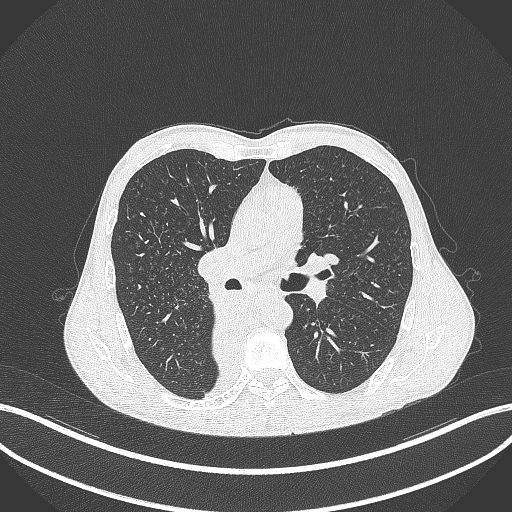
Chest CT, one axial slice. Slice 220 of 371 in the series (ordered by position). Lung window (W 1500 / L -600 HU). 512 × 512 image matrix, field of view 400 × 400 mm. Patient: male, 58 years. From the clinical record (not read from this slice): clinical TNM (as recorded): T3 N1 M1.
Outlined on this slice (bounding box drawn by a radiologist):
- lung tumour (recorded histology: squamous cell carcinoma): bounding box <198,287,248,377> (left, top, right, bottom; pixels)